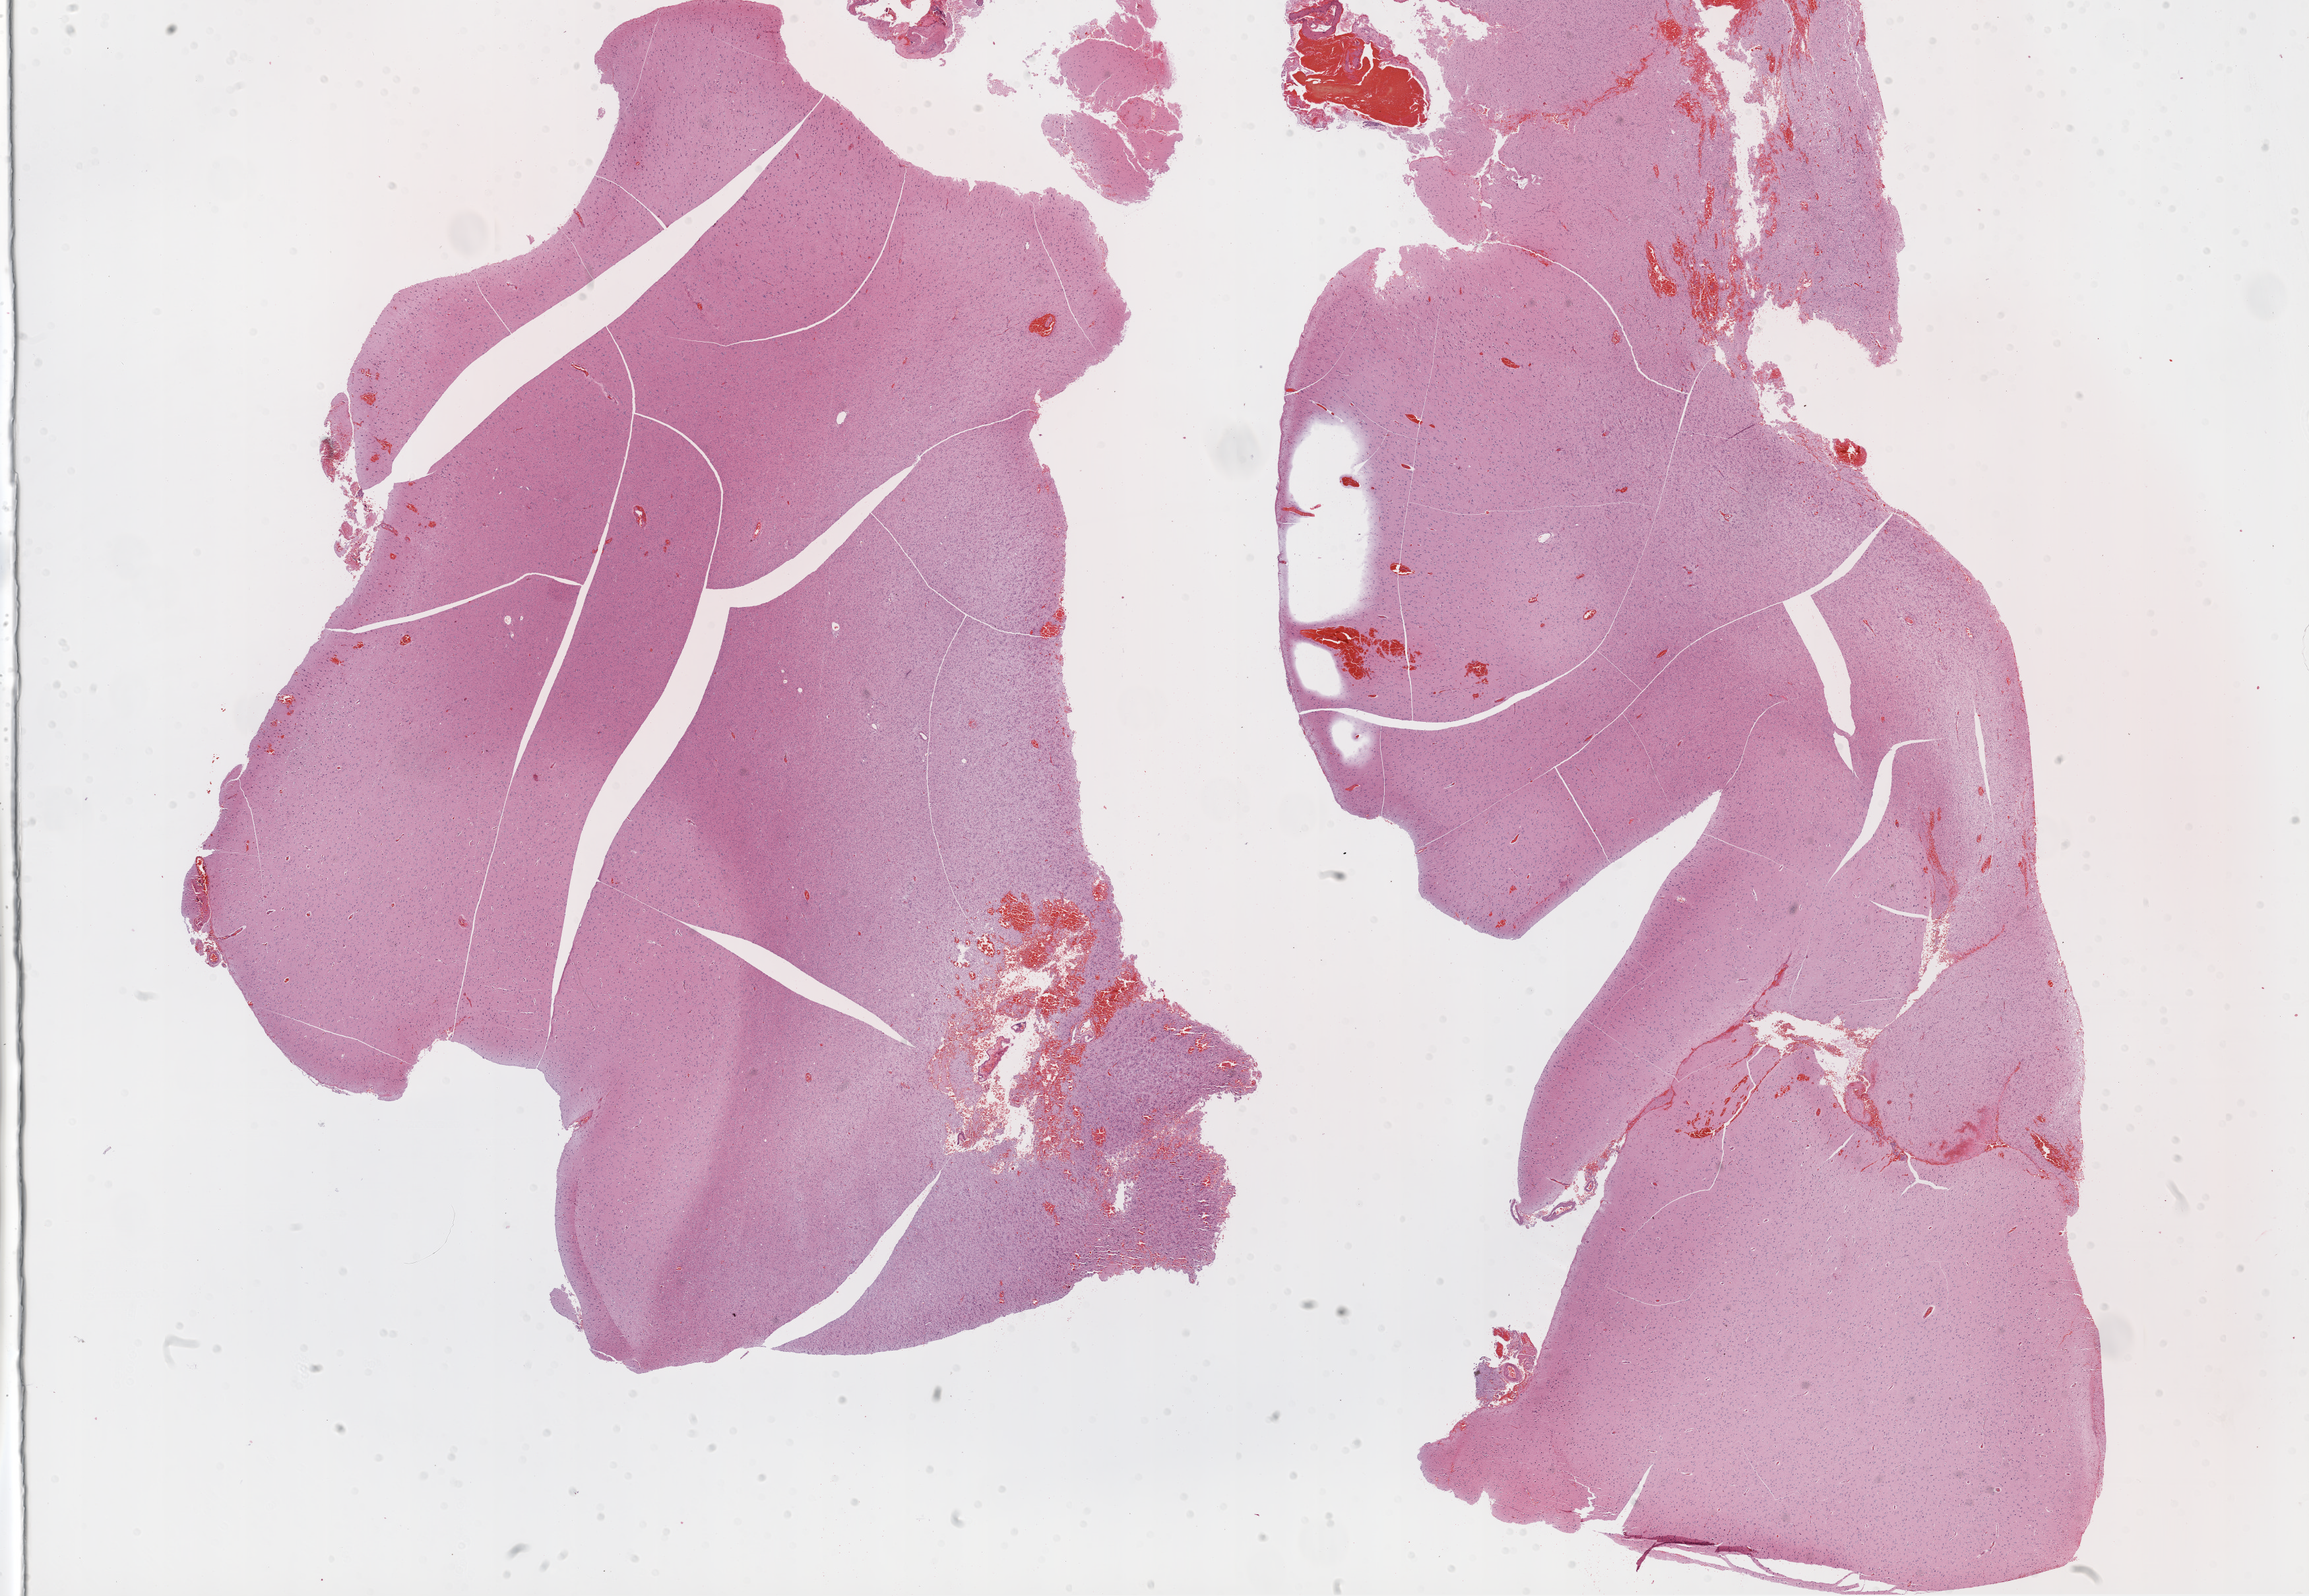
Digitized H&E tissue section (whole slide) — low-resolution overview of the scanned area, about 28.1 x 19.4 mm, formalin-fixed paraffin-embedded (FFPE) diagnostic section, sample: primary tumour, brain. Patient: male, age at initial diagnosis 71 years.
Histologic diagnosis: Glioblastoma.